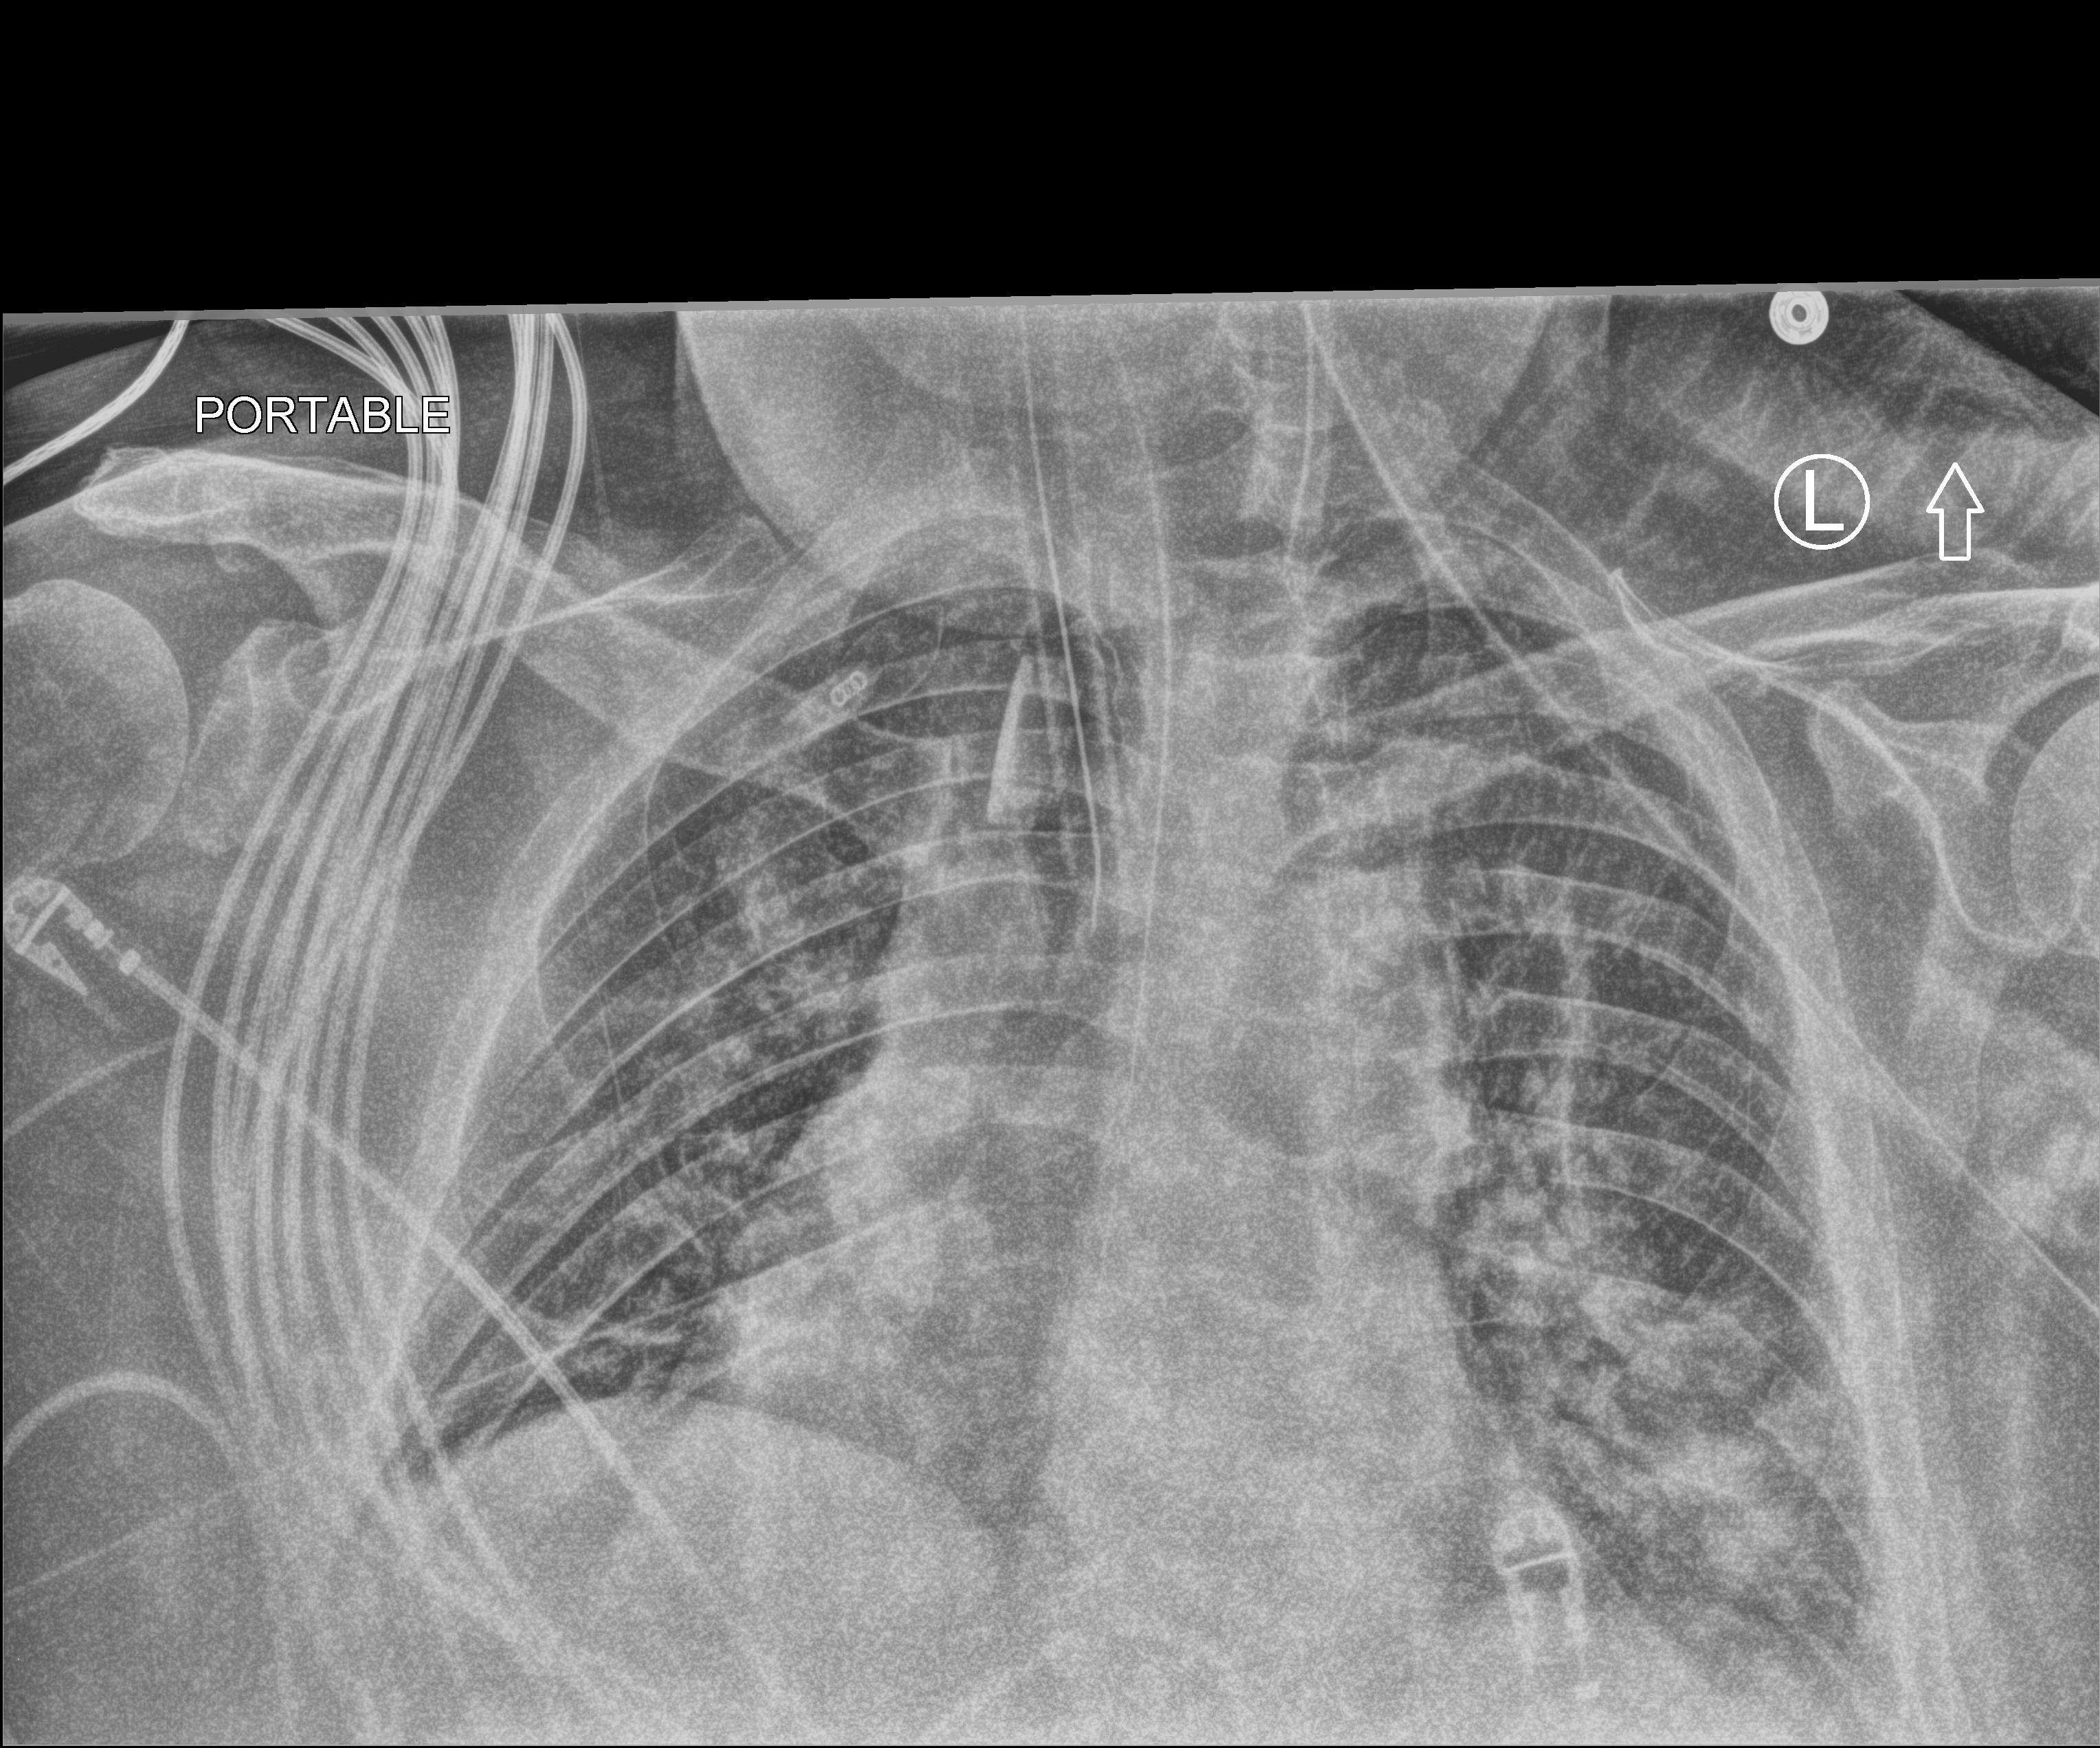
Bedside chest radiograph (computed radiography); anteroposterior (AP) projection. Patient hospitalised with COVID-19; male, aged 60–74 years.
From the hospital-stay record, not from the radiograph (when in the stay this image was taken is not recorded): admitted to intensive care during this hospital stay: yes.